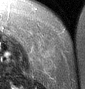
MRI of an extremity soft-tissue mass, one axial slice. Position 12 of 46 along the scan axis. T2-weighted fat-saturated. MR volume resampled by the dataset authors to the PET/CT grid (not the native acquisition matrix). 85 × 89 image matrix, field of view 83 × 87 mm. Female patient. From the clinical record (not read from this slice): histological type: leiomyosarcoma; grade: intermediate; site of the primary tumour: parascapusular.
Annotated regions visible in this slice (expert contour drawn on MRI and transferred to this co-registered scan by the dataset authors):
- gross tumour volume including surrounding oedema: bounding box [x1, y1, x2, y2] px = [32, 46, 62, 70]
- gross tumour volume (mass): [34, 48, 60, 67]